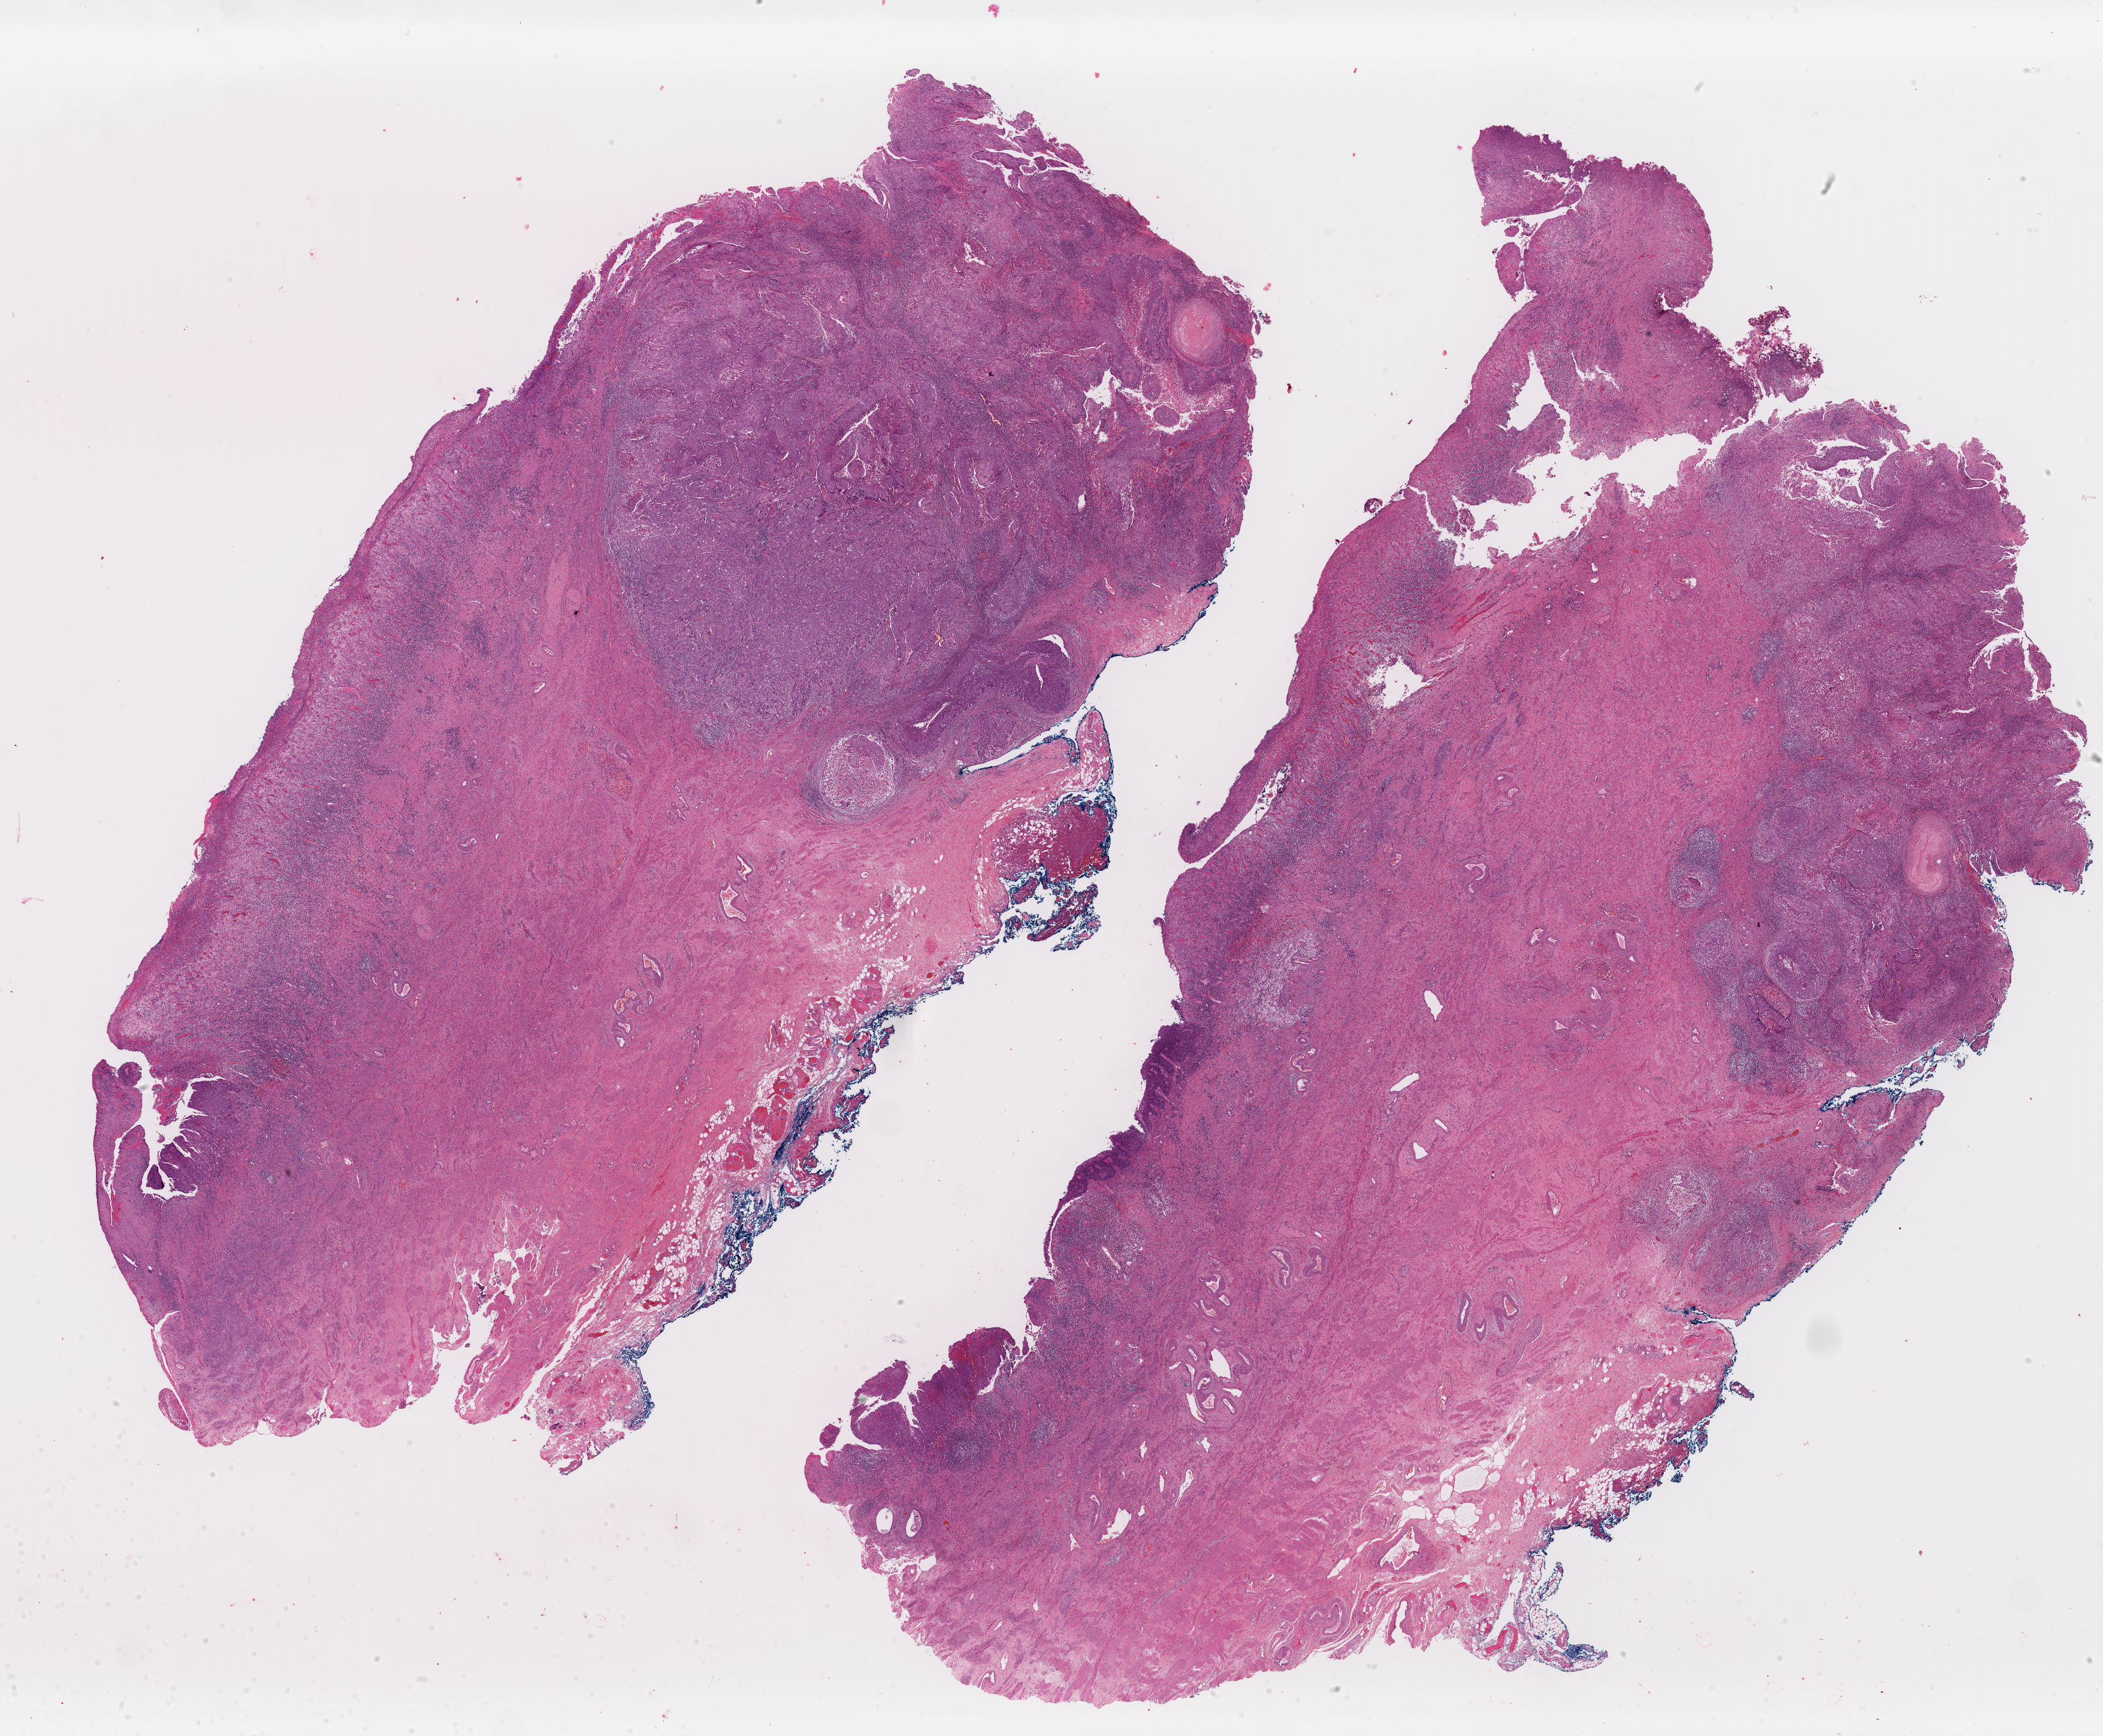
Digitized H&E-stained tissue section (whole slide), low-resolution overview of the scanned area, about 27.7 x 22.9 mm; FFPE section; primary tumour sample from the cervix. Female patient; age at initial diagnosis 75 years. Histologic grade: G3 (poorly differentiated).
- FIGO stage: IVA
- pathologic diagnosis: Squamous cell carcinoma, NOS (cervix uteri)
- lymph nodes positive (case pathology): 0 of 19 examined